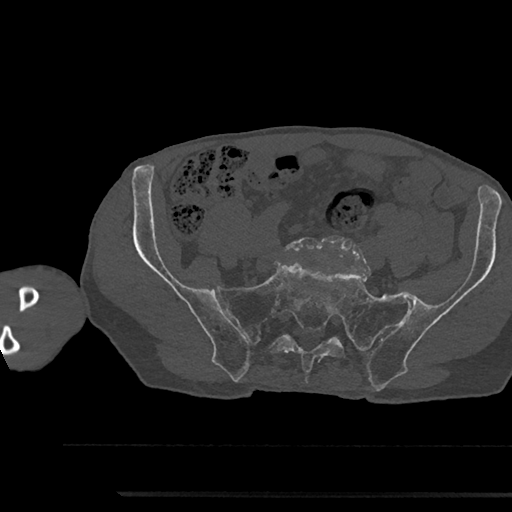
CT including the spine, one axial slice. Position 286 of 797 along the scan axis. Reconstruction kernel Br40s/3. 120 kVp. Bone window (W 1800 / L 400 HU). 0.5 mm slice thickness. 512 × 512 image matrix. Patient: male, 79 years. From the clinical record (not read from this slice): primary cancer: prostate.
Structures marked on this image (semi-automatically segmented with operator editing):
- L5 vertebra: bounding box (x1, y1, x2, y2) in pixels: (285, 238, 354, 253)